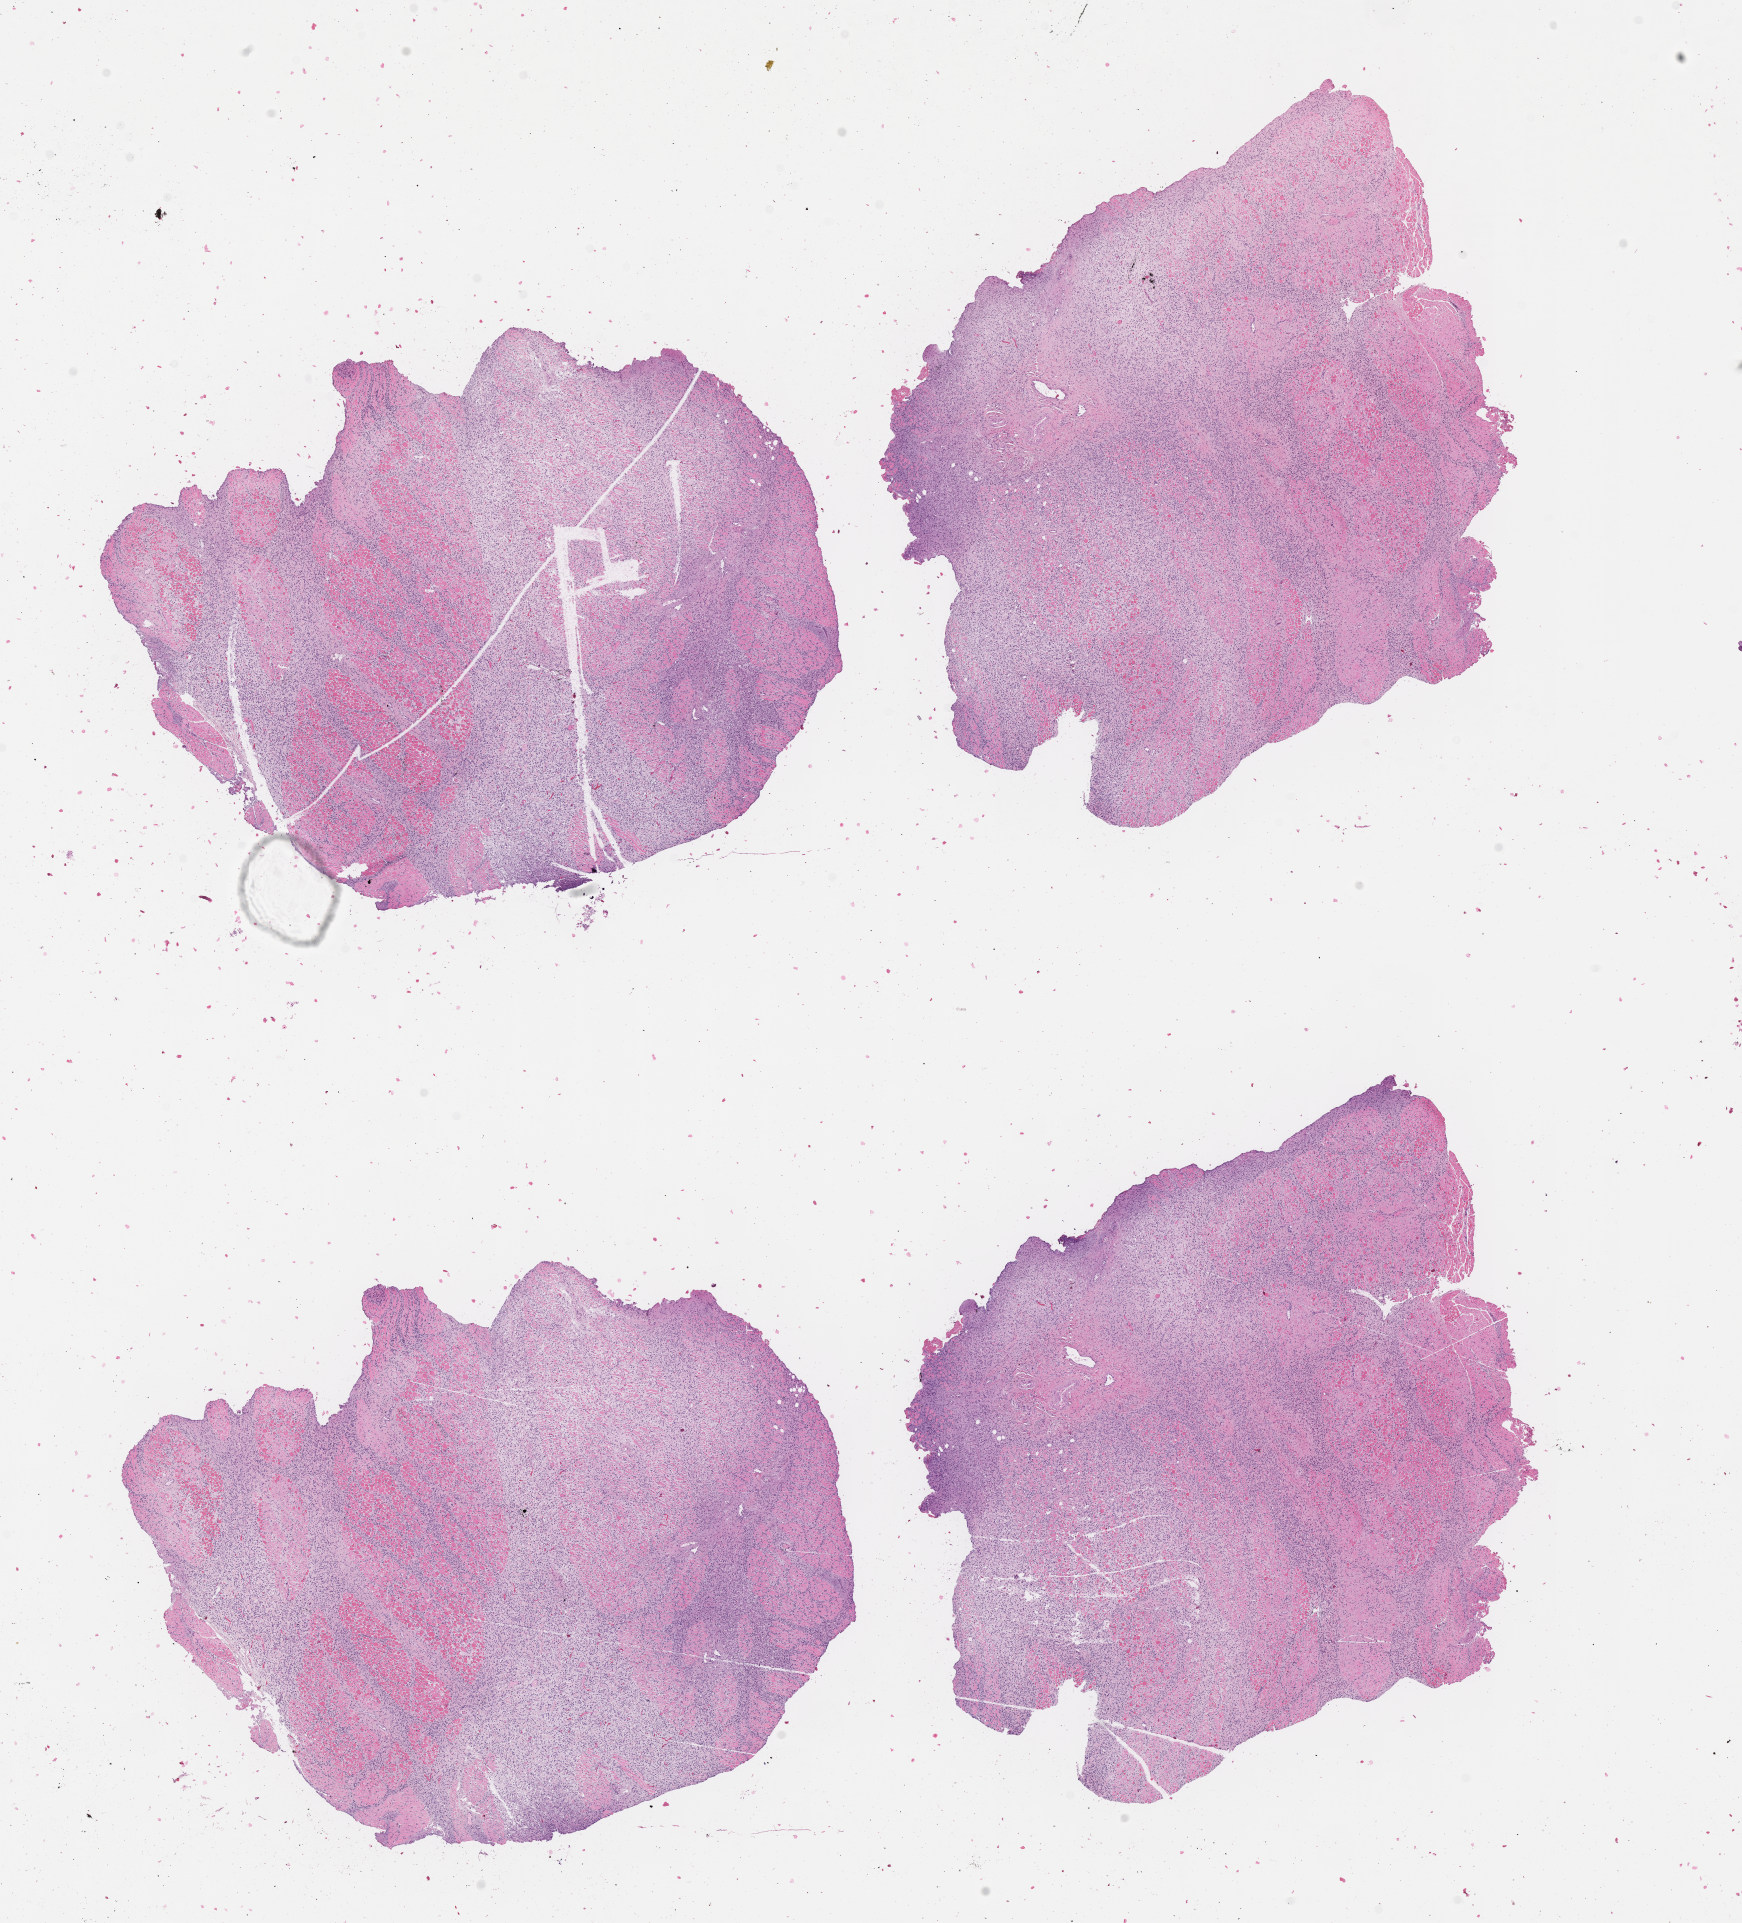
H&E whole-slide image of tumor tissue, low-resolution overview of the scanned area, about 14.1 x 15.6 mm; FFPE section; site: muscle, back-left. Patient: female, age 0.2 years at diagnosis.
Primary site (case record): chest Wall. Stage (as recorded): 3. Diagnosis: rhabdomyosarcoma; histological classification: embryonal rhabdomyosarcoma.